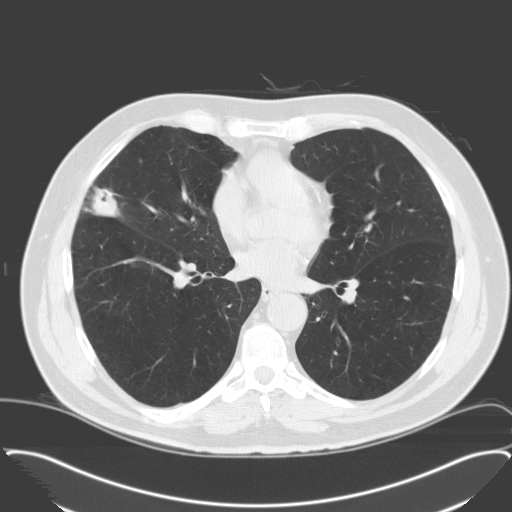
Low-dose screening chest CT, axial slice. Third screening round (two years after baseline). Lung window (W 1500 / L -600 HU). 3.2 mm slice thickness. Standard (soft-tissue) reconstruction kernel (C). Slice 90 of 174 in the series. 512 × 512 image matrix. Male, age 65 years at enrolment. Former smoker at enrolment.
- Expert reader's lesion annotation, bounding box <65,172,130,229> (left, top, right, bottom; pixels).
- The exam's reader record, not a measurement of the box and not confirmed to be the same lesion: non-calcified nodule or mass ≥4 mm, right middle lobe, 28 × 23 mm, spiculated (stellate) margins, soft tissue attenuation, pre-existing on the prior screen: no.
- Official screen result: positive, other.
- Participant outcome: lung cancer diagnosed 25 days after this screen — adenocarcinoma, NOS, right middle lobe, moderately differentiated (G2), stage IA (AJCC 6th edition), 25 mm at pathology.